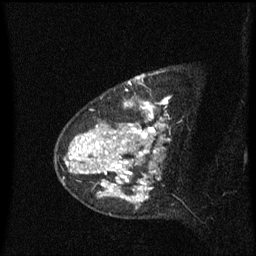
Breast MRI (dynamic contrast-enhanced), one sagittal slice; position 45 of 60 along the scan axis; dynamic contrast-enhanced series, image 2 of 3 at this slice position (ordered by acquisition); 1.5 T; TE 4.2 ms, TR 8.4 ms; 2 mm slice thickness; 256 × 256 image matrix, field of view 200 × 200 mm. Patient: female, 48 years. Case-level facts recorded for this patient, not image findings: setting: breast cancer imaged before/during neoadjuvant chemotherapy; receptor status: HR-positive, HER2-negative.
Structures marked on this image (semi-automatically segmented with operator editing):
- analysis volume of interest (the breast-tissue region the enhancement analysis was run in; not a lesion): box from (x=80, y=78) to (x=171, y=219) px
- tumour enhancement mask (voxels above the 70 % enhancement threshold inside the analysis volume of interest): (x=80, y=78)–(x=165, y=201)